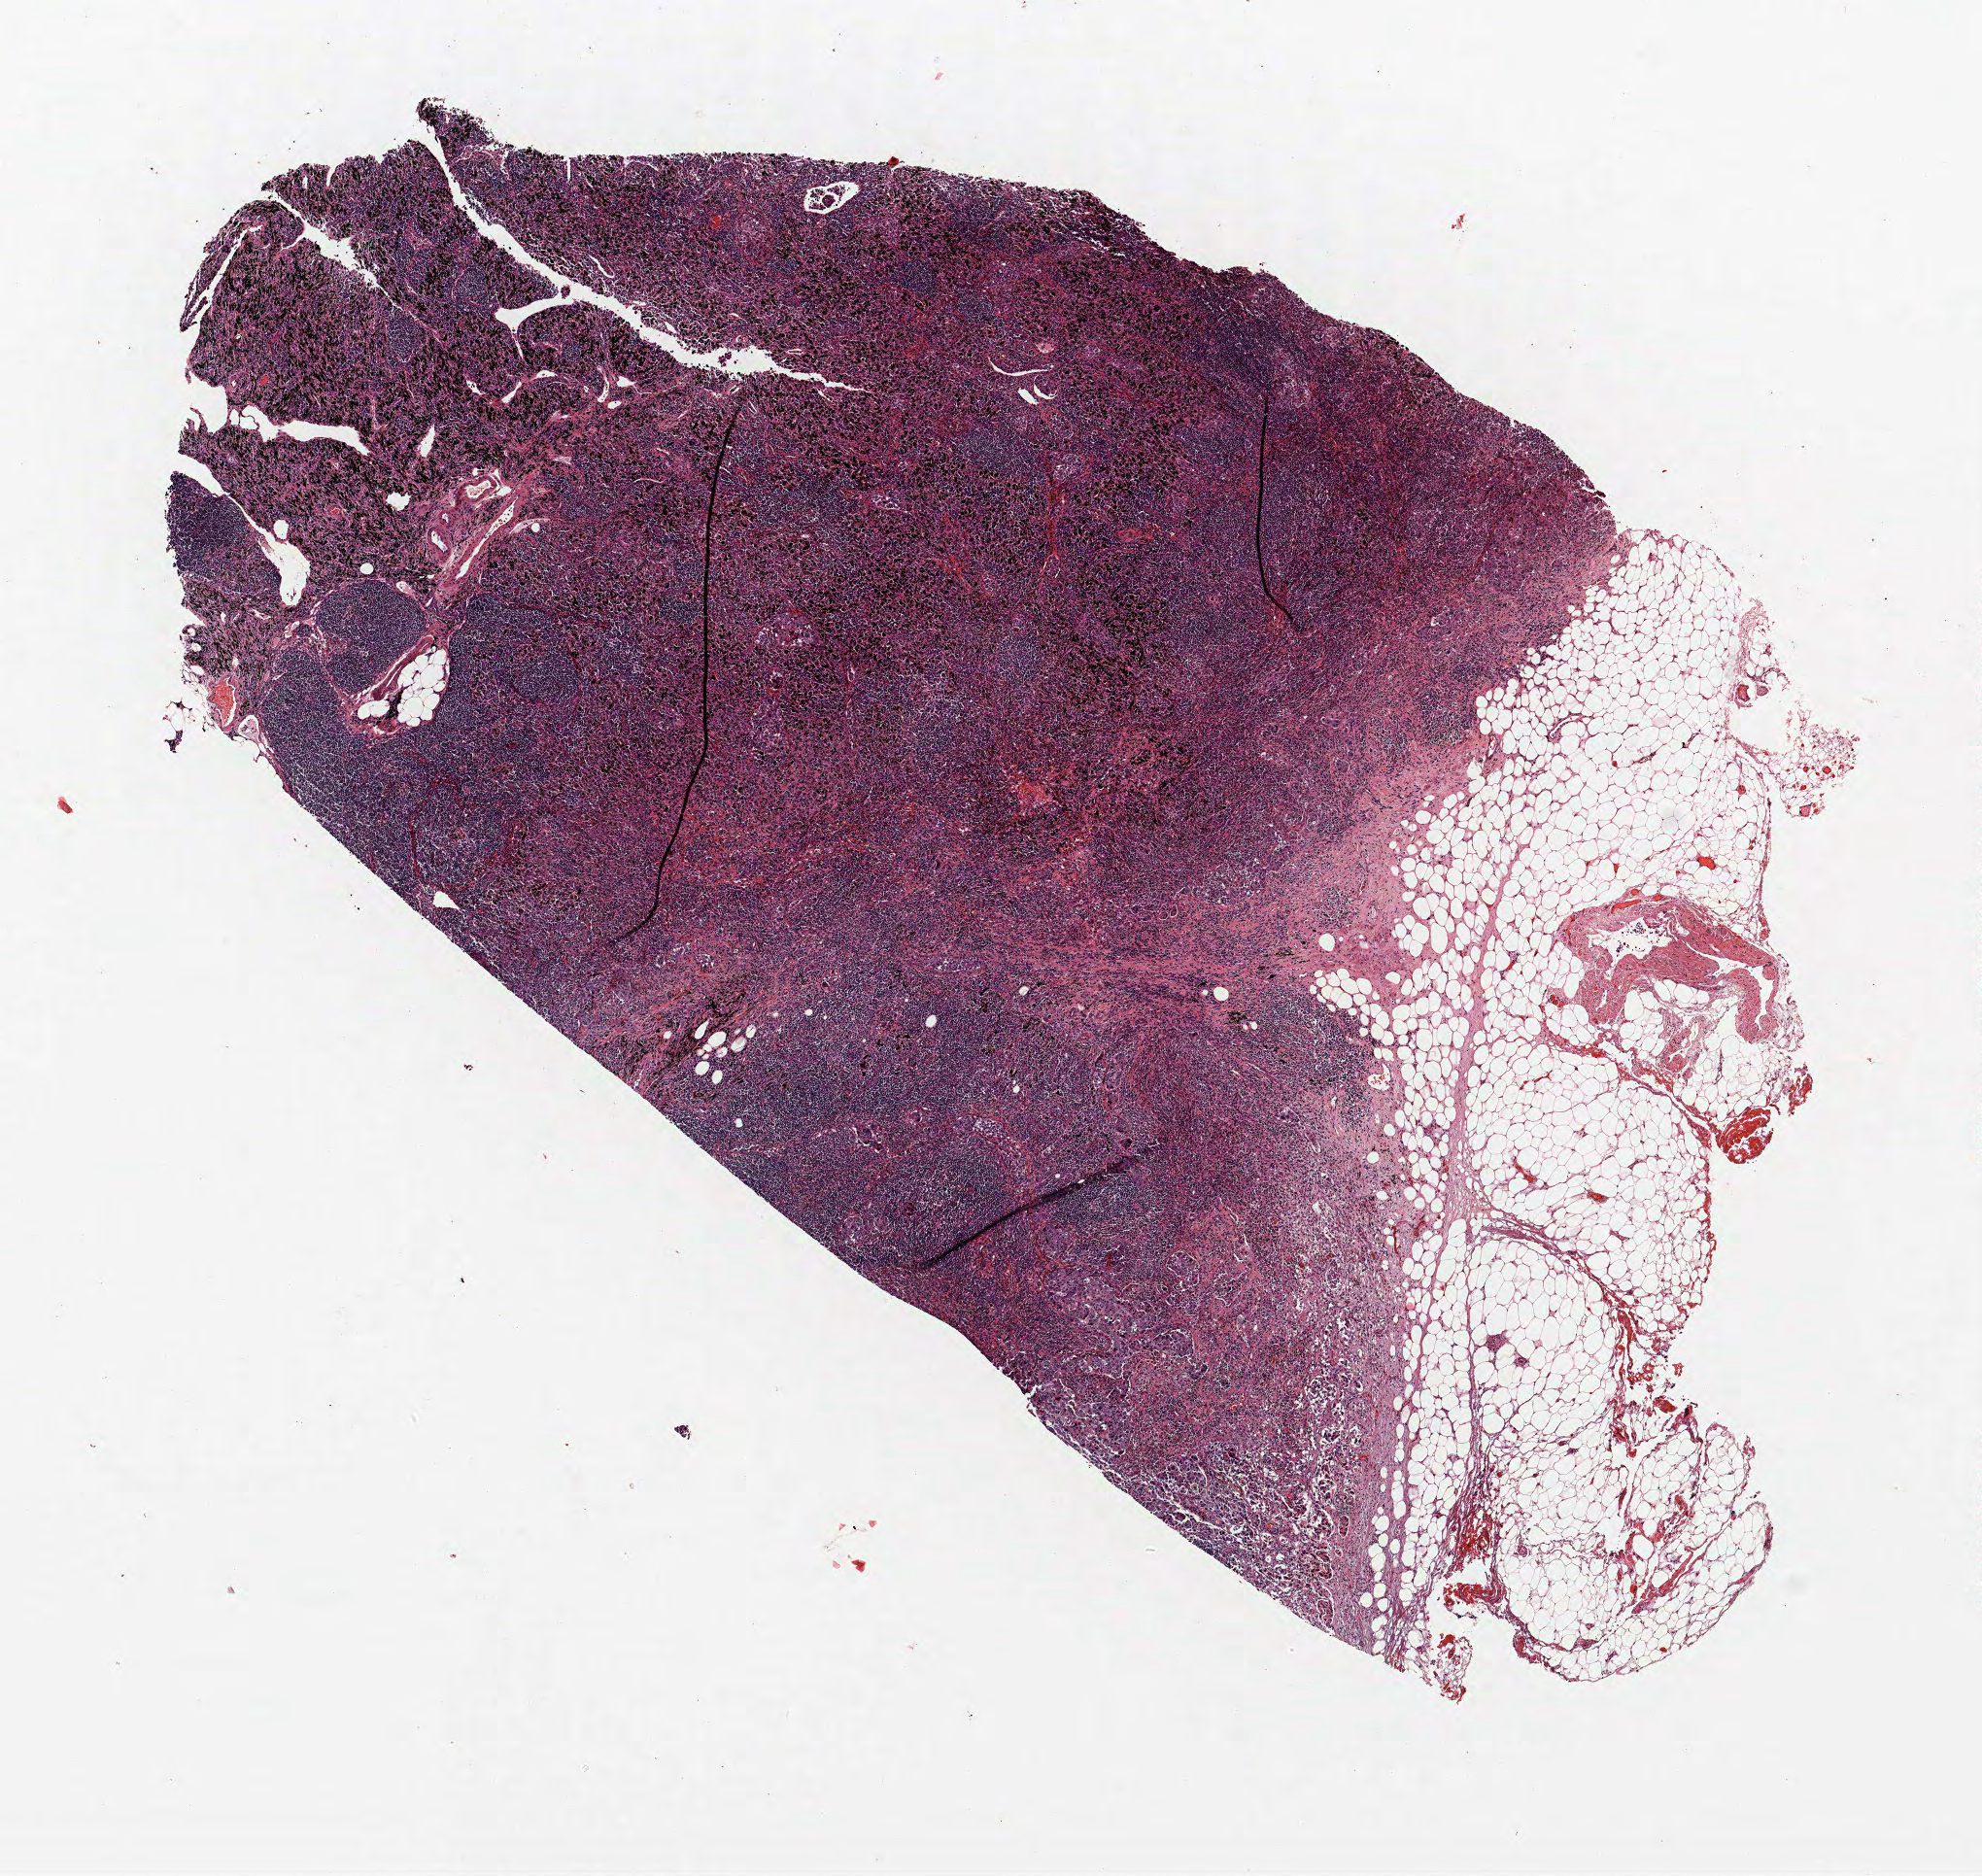
Whole-slide histology image, Hematoxylin and eosin (H&E) stained, shown as a low-resolution overview of the whole scanned area (about 8.2 x 7.7 mm); FFPE section; lung. Male, age 73 at enrolment. Current smoker at enrolment.
Participant's lung-cancer diagnosis: Adenocarcinoma, NOS (ICD-O-3 8140/3).